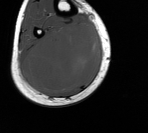
MRI of an extremity soft-tissue mass, one axial slice; position 50 of 76 along the scan axis; MR volume resampled by the dataset authors to the PET/CT grid (not the native acquisition matrix); 148 × 133 image matrix. Male patient. Case-level facts recorded for this patient, not image findings: histological type: liposarcoma - round cell; grade: high; site of the primary tumour: right calf.
Annotated regions visible in this slice (expert contour drawn on MRI and transferred to this co-registered scan by the dataset authors):
- gross tumour volume (mass): bounding box [x1, y1, x2, y2] px = [22, 23, 101, 93]